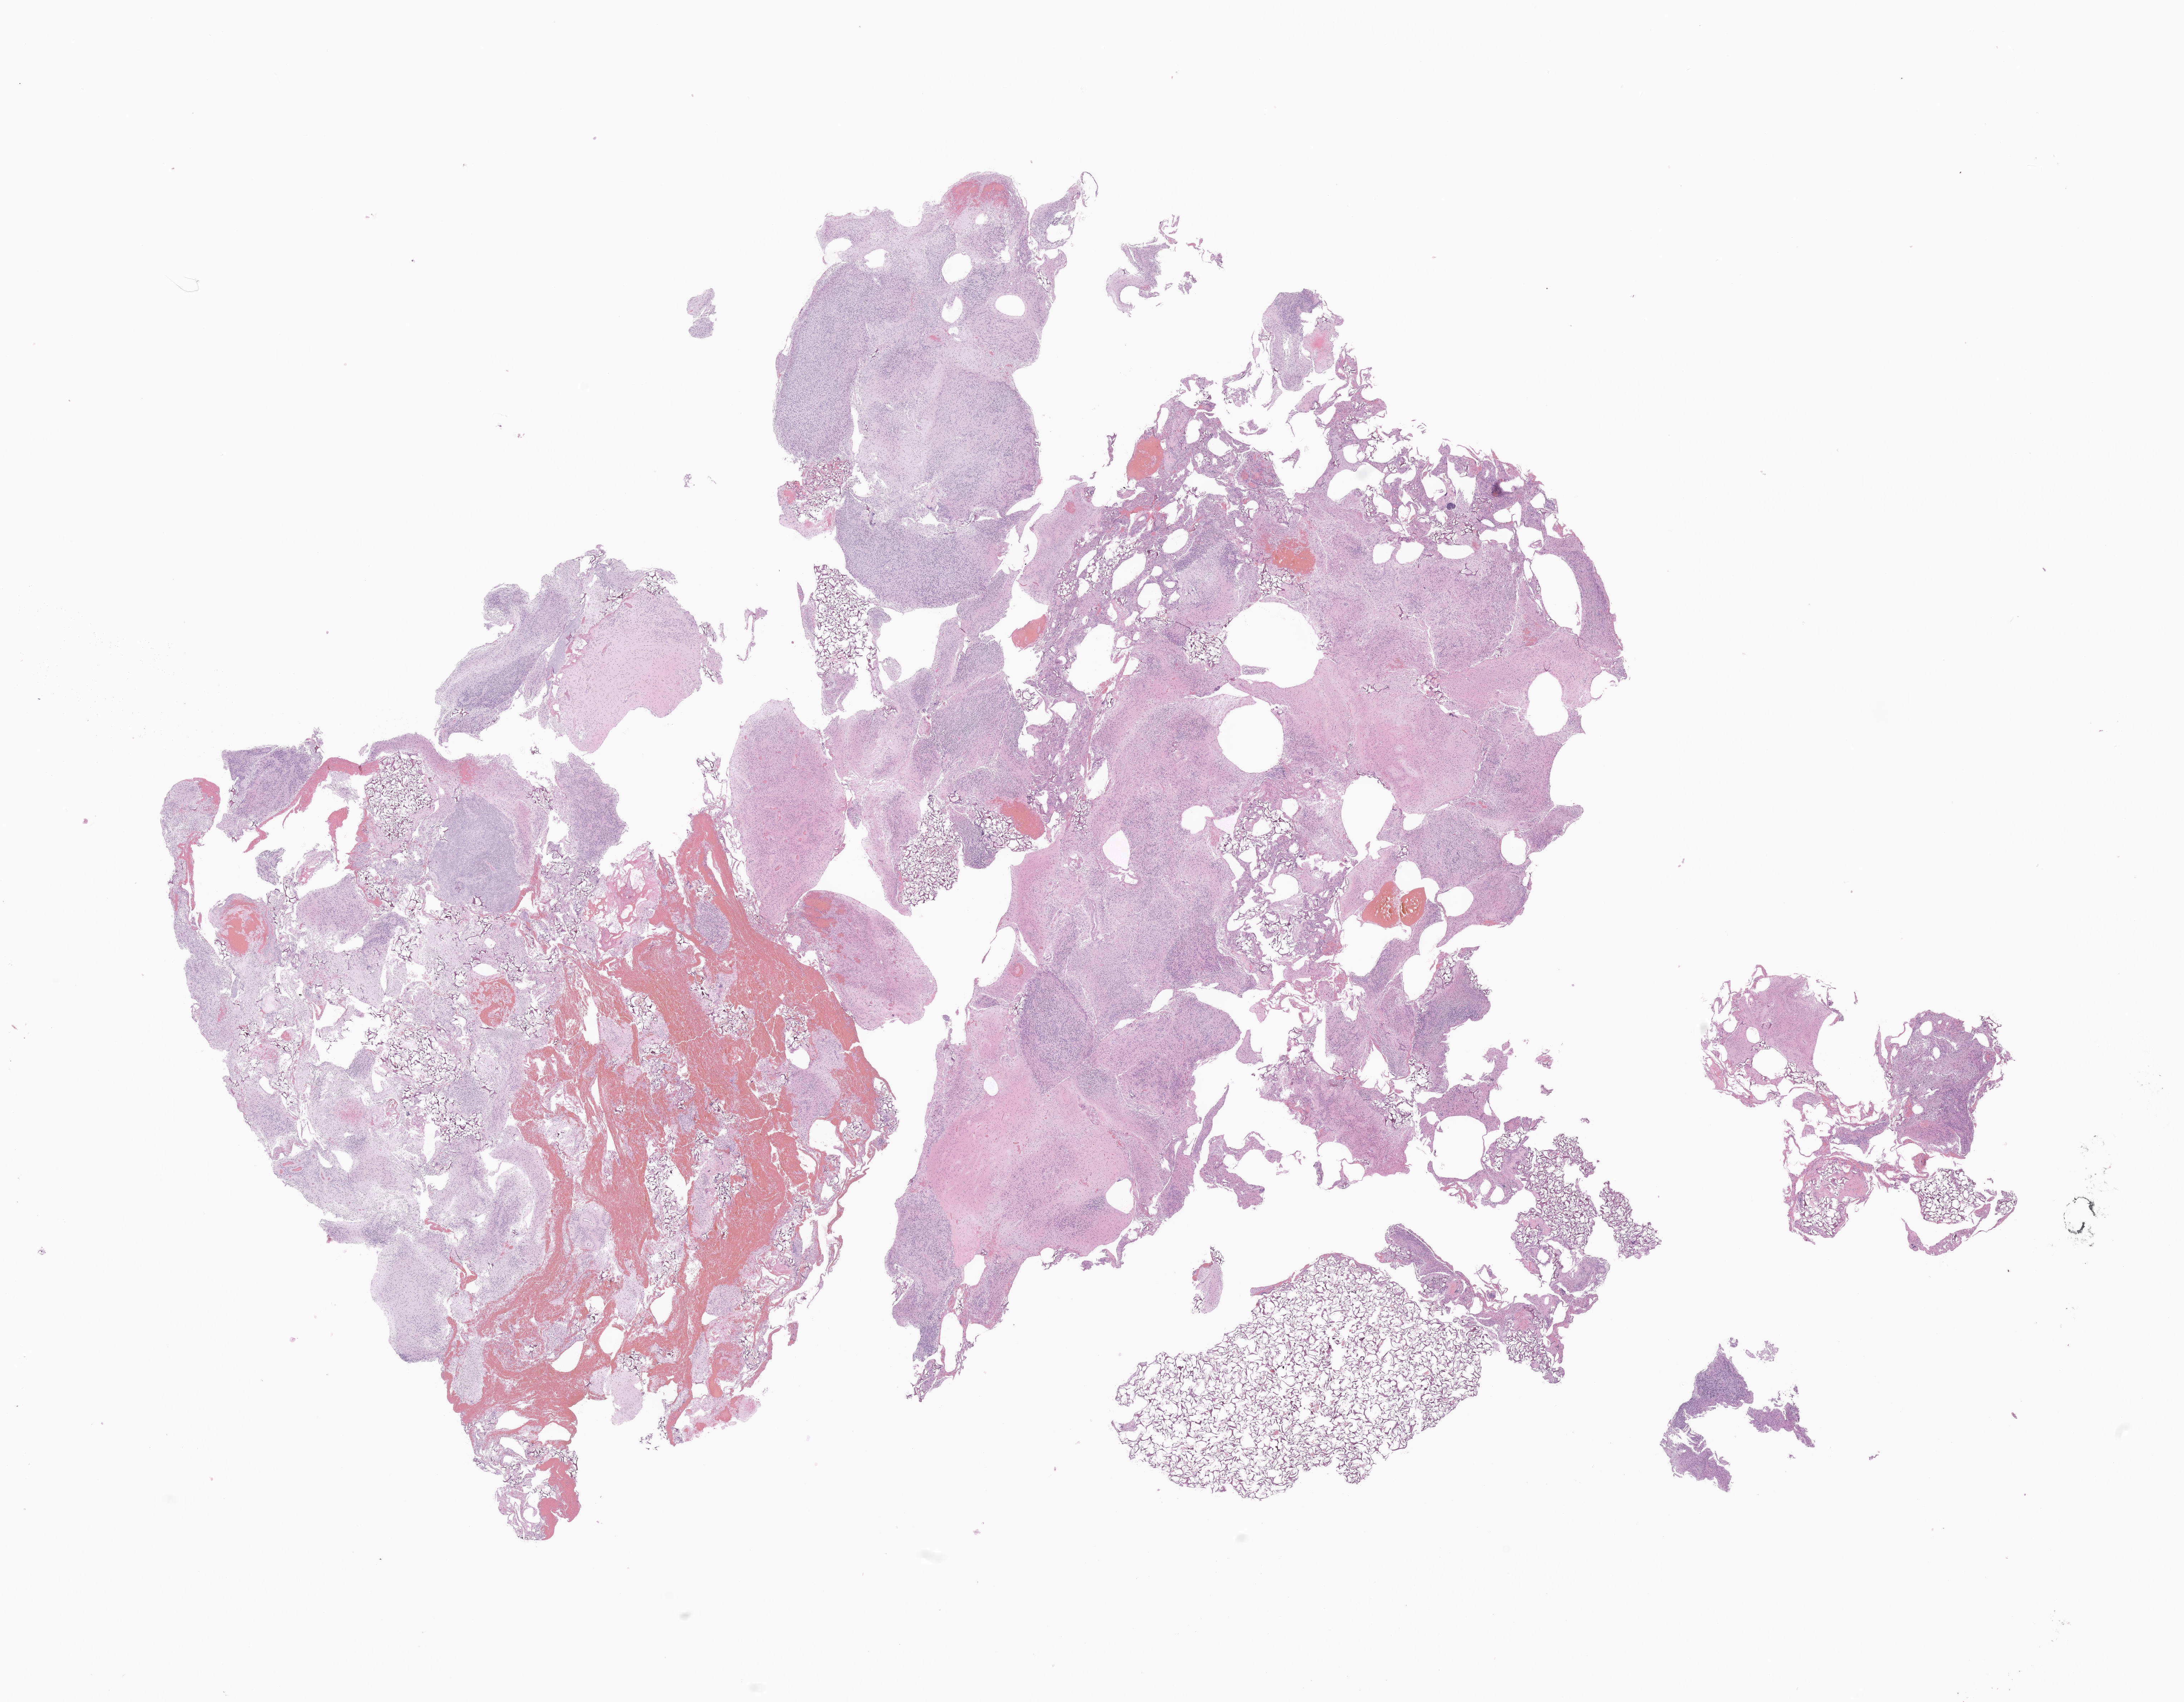
Whole-slide image, hematoxylin and eosin (H&E) stain of tumor tissue from the brain — low-resolution overview of the scanned area, about 25.8 x 20.1 mm; formalin-fixed, paraffin-embedded (FFPE) tissue. Patient male; age 900 days (about 2.5 years).
- diagnosis: Ependymoma, NOS